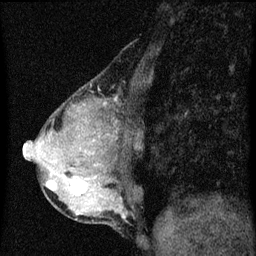
Breast MRI (dynamic contrast-enhanced), one sagittal slice; position 20 of 60 along the scan axis; dynamic contrast-enhanced series, image 2 of 3 at this slice position (ordered by acquisition); 1.5 T; TE 4.2 ms, TR 8 ms; 2 mm slice thickness; 256 × 256 image matrix. Female patient, age 49 years.
Outlined on this slice (semi-automatically segmented with operator editing):
- analysis volume of interest (the breast-tissue region the enhancement analysis was run in; not a lesion): bounding box (x1, y1, x2, y2) in pixels: (44, 174, 89, 201)
- tumour enhancement mask (voxels above the 70 % enhancement threshold inside the analysis volume of interest): (46, 180, 87, 195)